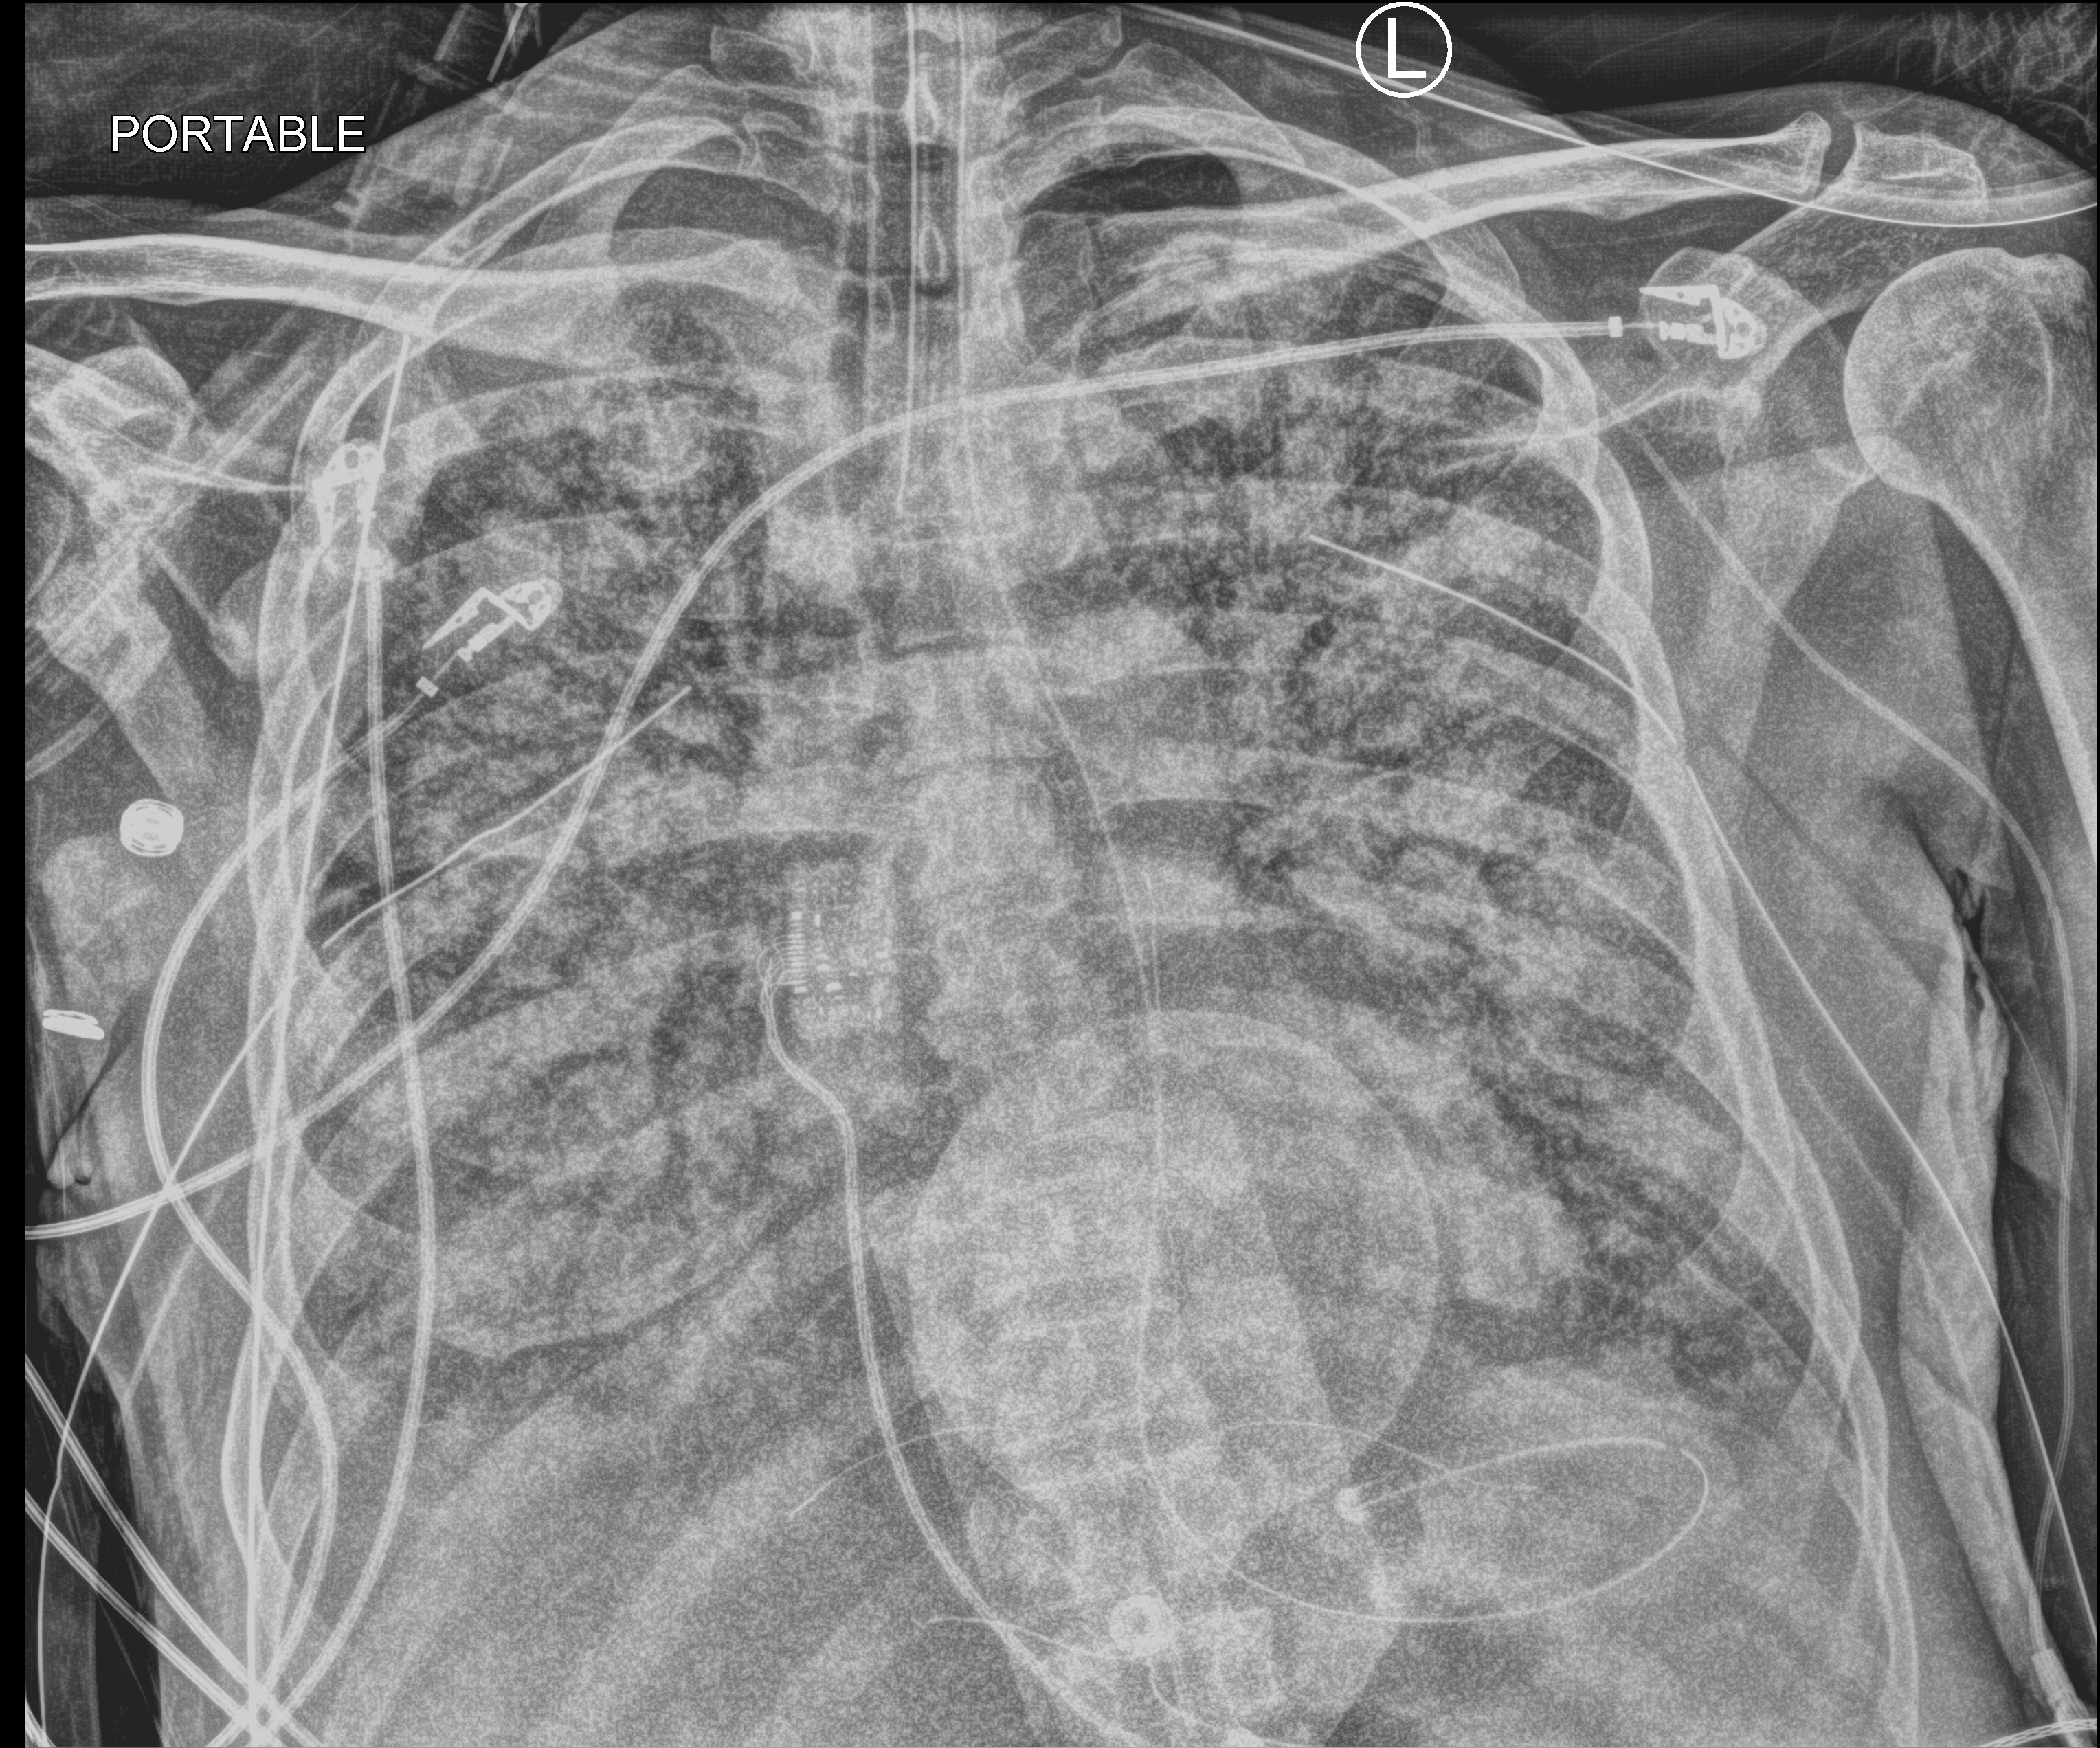
Bedside chest radiograph (computed radiography); anteroposterior (AP) projection. Patient hospitalised with COVID-19; male, aged 60–74 years.
From the hospital-stay record, not from the radiograph (when in the stay this image was taken is not recorded): length of hospital stay: 31 days.